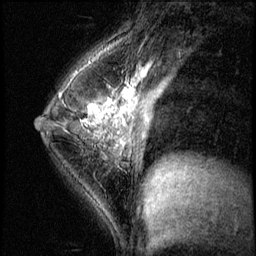
Breast MRI (dynamic contrast-enhanced), one sagittal slice; position 37 of 56 along the scan axis; 3 images stored at this slice position (order not interpretable as contrast timing); 1.5 T; TE 4.2 ms, TR 8.7 ms; 2.5 mm slice thickness; 256 × 256 image matrix, field of view 180 × 180 mm. Patient: female, 35 years. Case-level facts recorded for this patient, not image findings: setting: breast cancer imaged before/during neoadjuvant chemotherapy; receptor status: HER2-positive.
Annotated regions visible in this slice (semi-automatic segmentation, software-assisted and operator-edited):
- analysis volume of interest (the breast-tissue region the enhancement analysis was run in; not a lesion): bounding box (x1, y1, x2, y2) in pixels: (58, 84, 138, 186)
- tumour enhancement mask (voxels above the 140 % enhancement threshold inside the analysis volume of interest): (58, 103, 101, 137)